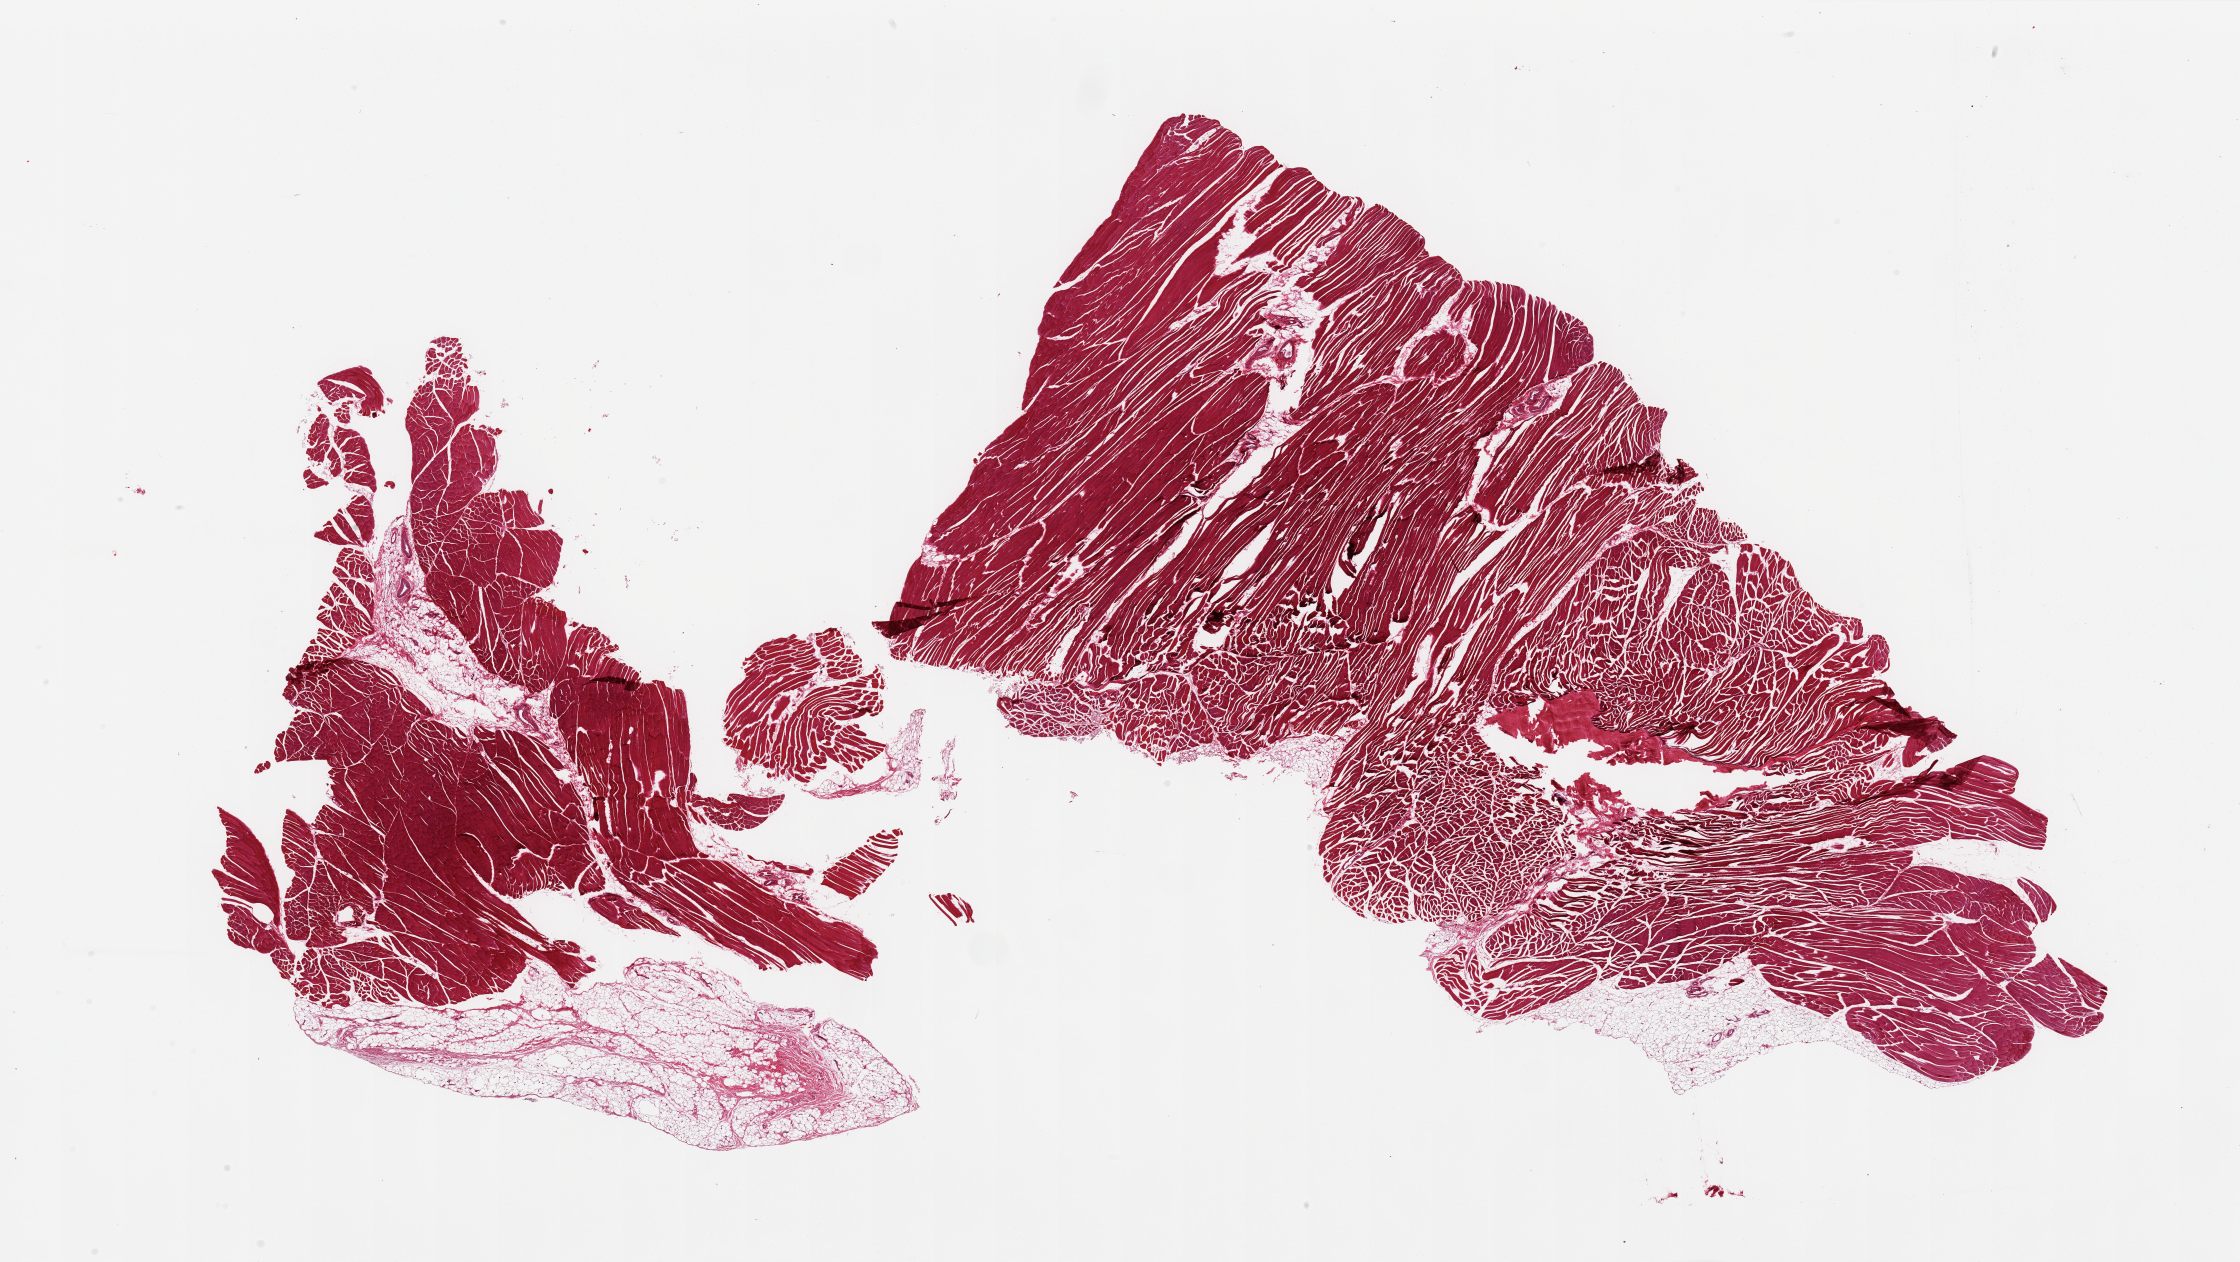
Whole-slide image, haematoxylin and eosin stain — shown as a low-resolution overview of the whole scanned area (about 35.4 x 20.0 mm, acquisition: 20x scan). PAXgene-fixed, paraffin-embedded tissue. Section of skeletal muscle (target tissue). Donor tissue sample.
* reviewer comment on this tissue sample: 2 pieces; 1 has 30% external fat